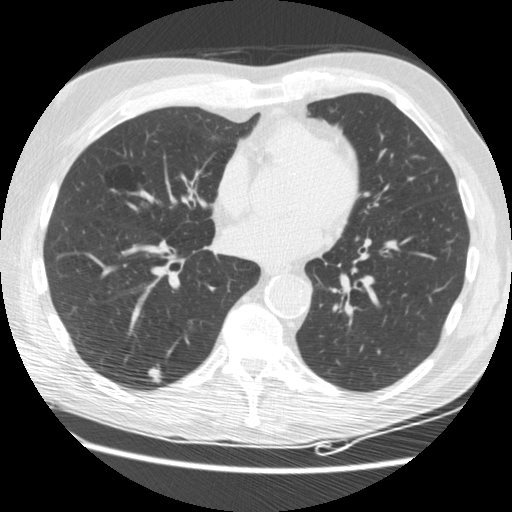
Chest CT (low-dose screening protocol), one axial image. Third annual screen. Lung window (W 1500 / L -600 HU). Slice 100 of 176 in the series. Male participant, aged 62 years at enrolment. Current smoker at enrolment.
Expert reader's lesion annotation, bounding box [x1, y1, x2, y2] px = [140, 354, 182, 395]. The screening reader recorded 3 non-calcified nodules or masses ≥4 mm on this exam; which of them this box marks is not recorded. Later outcome: lung cancer diagnosed 33 days after this screen — adenocarcinoma, NOS, right lower lobe, moderately differentiated (G2), stage IIIB (AJCC 6th edition), 15 mm at pathology.